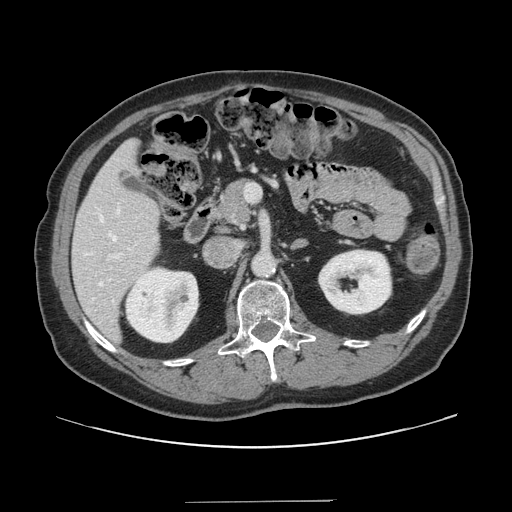
Contrast-enhanced abdominal CT, one axial slice. Position 72 of 151 along the scan axis. Soft-tissue window (W 400 / L 40 HU). 512 × 512 image matrix, field of view 399 × 399 mm. Male patient, age 63 years. Case-level facts recorded for this patient, not image findings: diagnosis: colorectal cancer liver metastases, imaged before liver resection; multiple liver metastases: no; largest metastasis: 2.1 cm; disease in both lobes: no.
Structures marked on this image (outlined manually by an expert reader):
- hepatic veins: bounding box [x1, y1, x2, y2] px = [99, 209, 120, 286]
- liver: [73, 140, 160, 341]
- planned liver remnant (the part of the liver to remain after resection): [73, 141, 160, 341]
- portal vein (with intrahepatic branches): [108, 184, 260, 260]